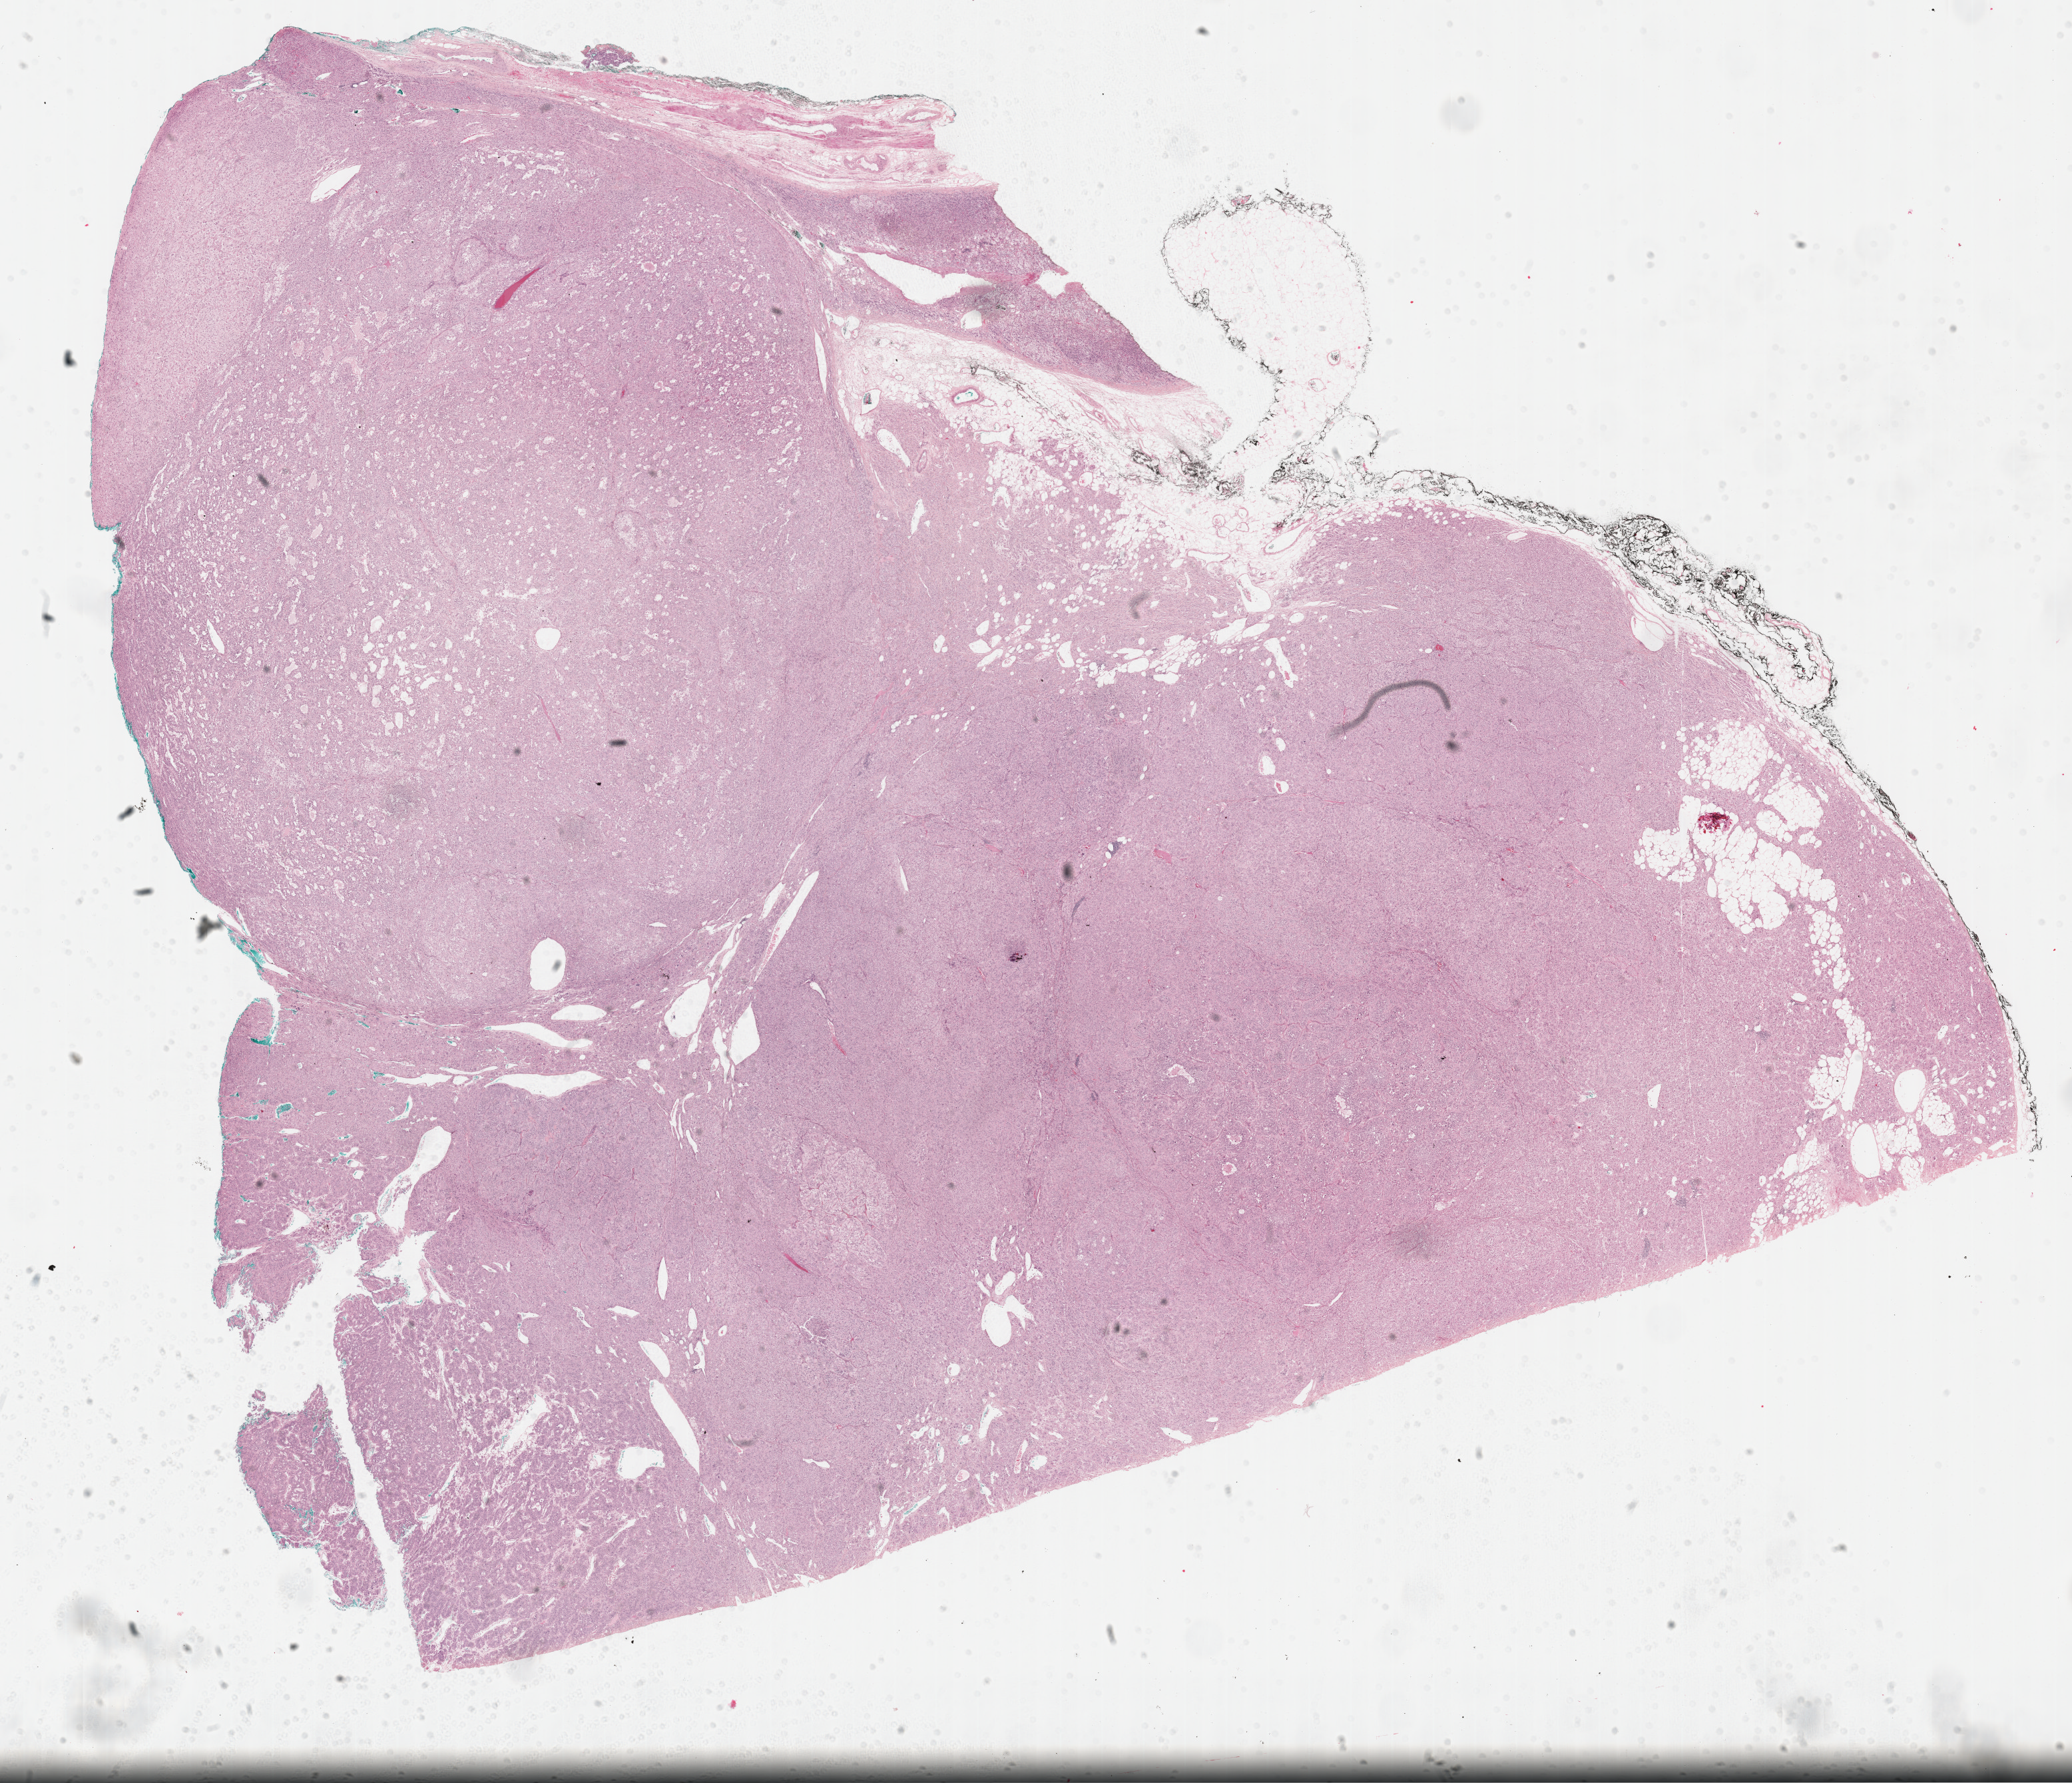
Whole-slide histology image, Hematoxylin and eosin (H&E) stained — whole scanned area (about 25.2 x 21.7 mm, slide scanned at 40x) shown as a low-resolution overview. FFPE section. Primary tumour sample from the adrenal cortex. Female patient; age at initial diagnosis 69 years.
Pathologic diagnosis: Adrenal cortical carcinoma.